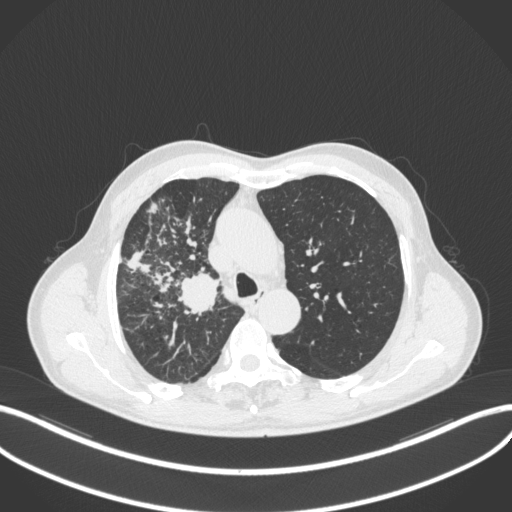
Chest CT, one axial slice; slice 343 of 490 in the series (ordered by position); reconstruction kernel B31f; 120 kVp; lung window (W 1500 / L -600 HU); 1 mm slice thickness; 512 × 512 image matrix. Patient: male, 69 years. From the clinical record (not read from this slice): clinical TNM (as recorded): T2a N0 M0.
Outlined on this slice (rectangle marked by the reading radiologist):
- lung tumour (recorded histology: adenocarcinoma): bounding box <174,271,226,319> (left, top, right, bottom; pixels)